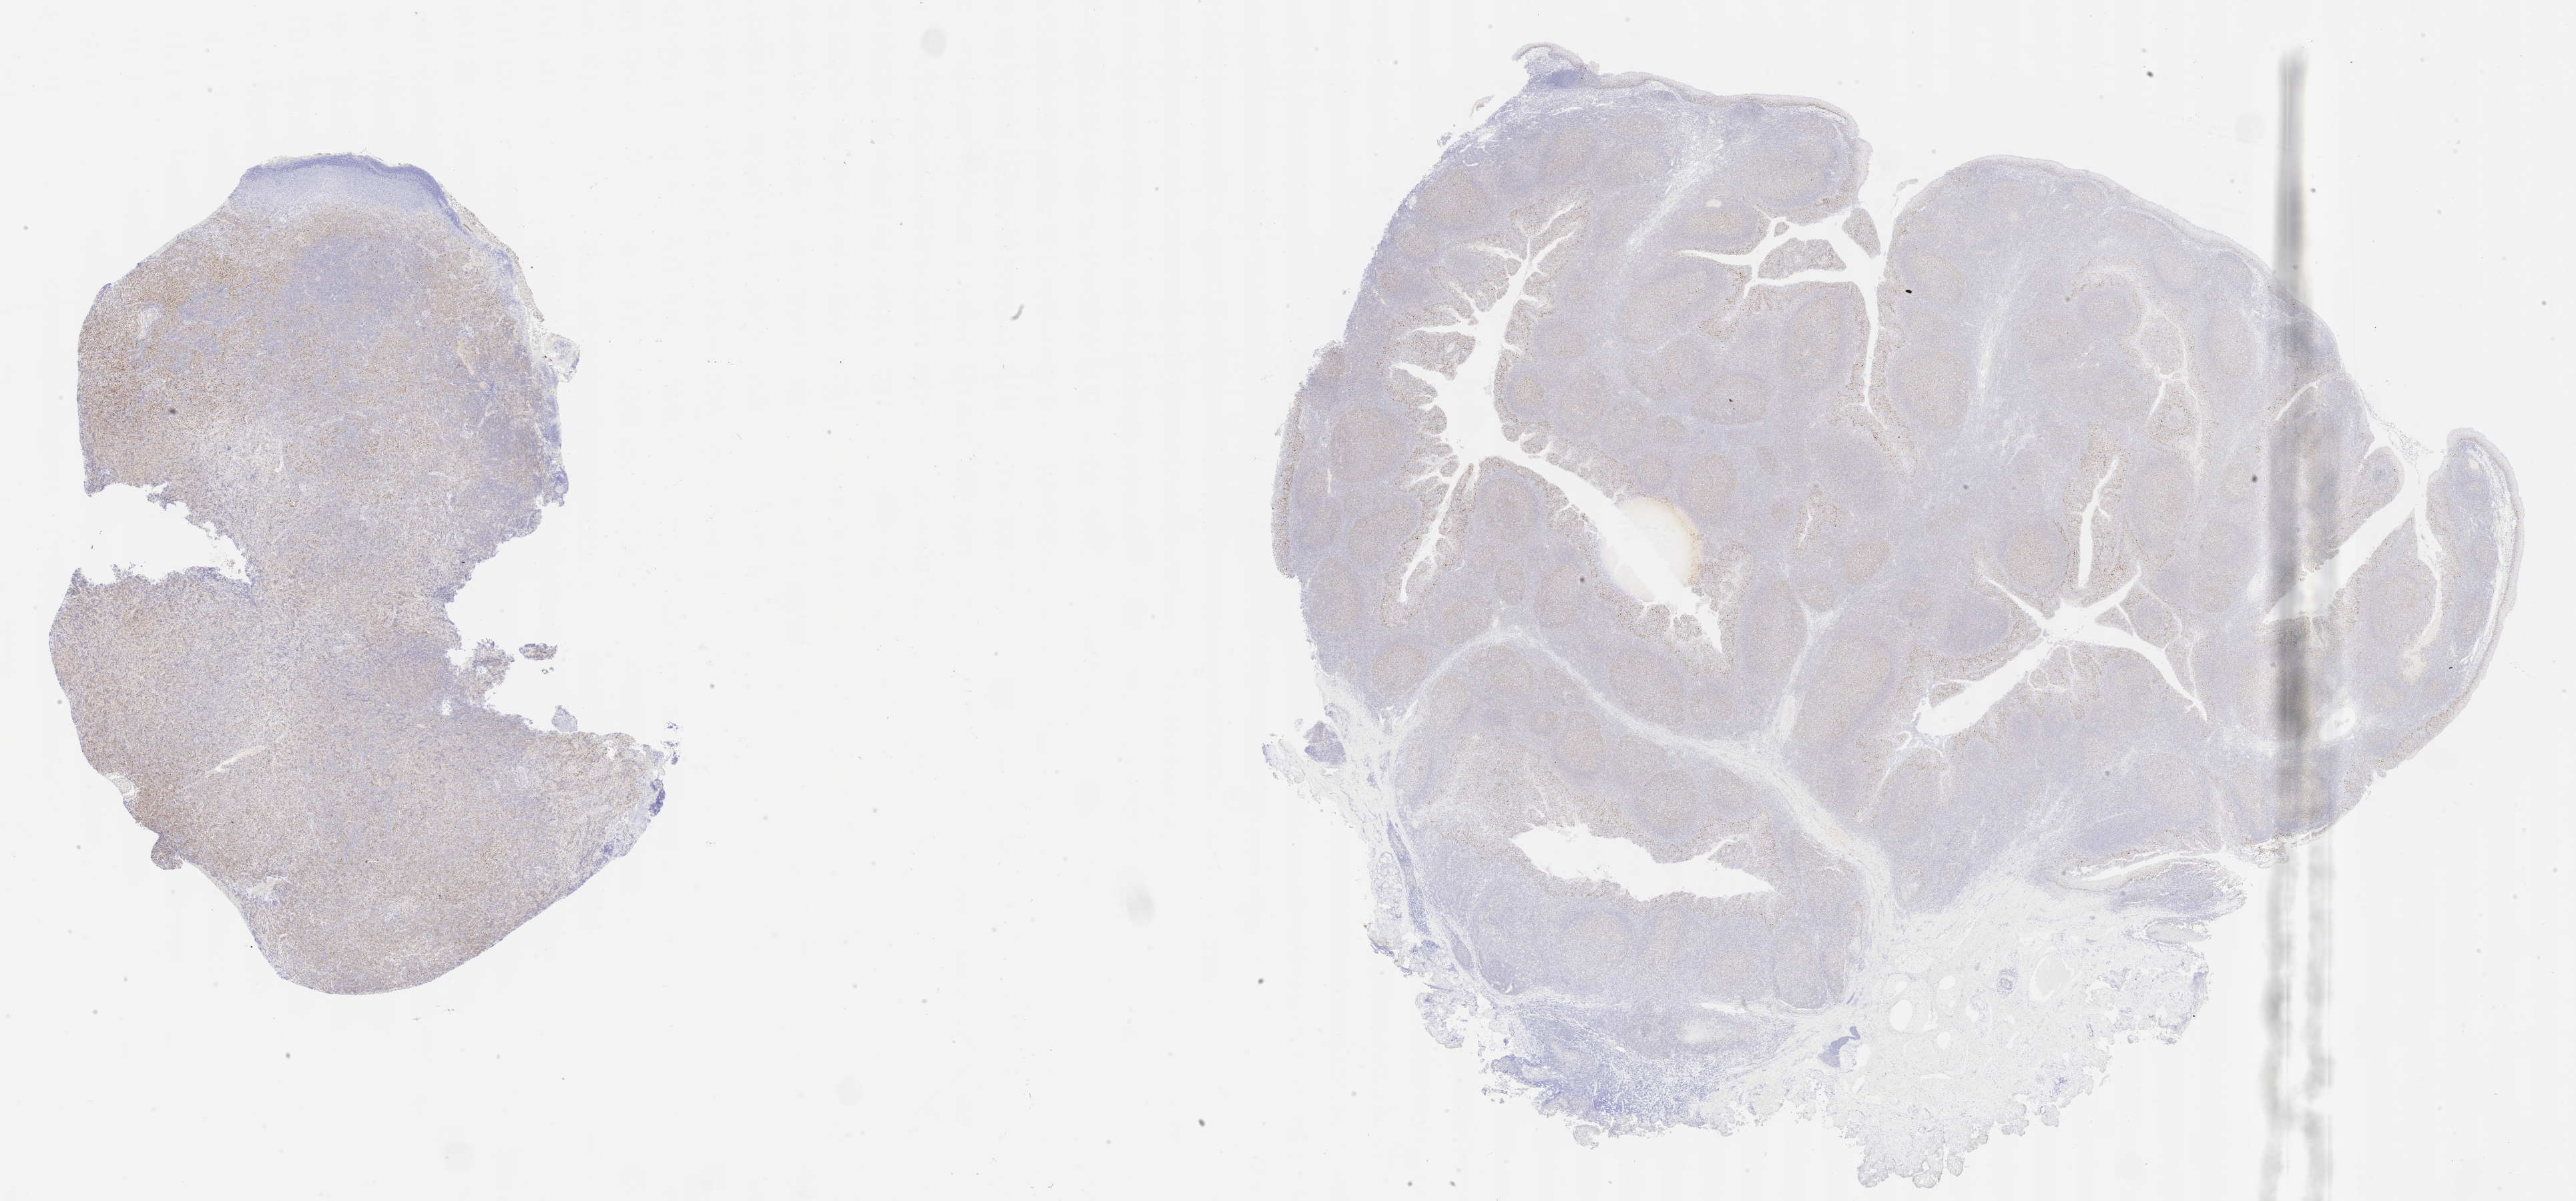
Immunohistochemistry (IHC) whole-slide image stained for p53, whole scanned area (about 31.2 x 14.5 mm) shown as a low-resolution overview; specimen: tumor tissue. Male patient; age at initial diagnosis 7 years.
• diagnosis: Diffuse large B-cell lymphoma, NOS